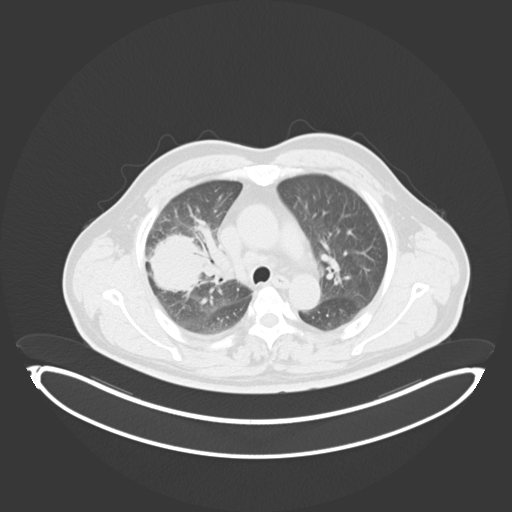
Chest CT, one axial slice. Position 219 of 284 along the scan axis. Reconstruction kernel B30f. 120 kVp. Lung window (W 1500 / L -600 HU). 3 mm slice thickness. 512 × 512 image matrix, field of view 500 × 500 mm. Patient: male, 55 years. From the clinical record (not read from this slice): clinical TNM (as recorded): T3 N2 M1.
Structures marked on this image (bounding box drawn by a radiologist):
- lung tumour (recorded histology: adenocarcinoma): bounding box [x1, y1, x2, y2] px = [145, 229, 211, 294]